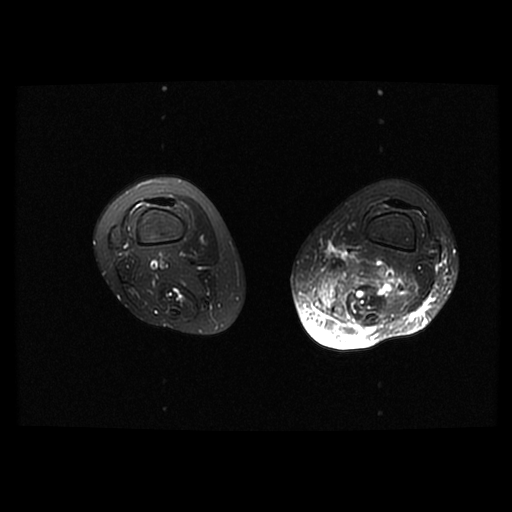
MRI of an extremity soft-tissue mass, one axial slice. Position 16 of 42 along the scan axis. T2-weighted fat-saturated. 6 mm slice thickness. 512 × 512 image matrix, field of view 420 × 420 mm. Female patient. Case-level facts recorded for this patient, not image findings: histological type: pleomorphic leiomyosarcoma; grade: high; site of the primary tumour: left thigh.
Annotated regions visible in this slice (outlined manually by an expert reader):
- gross tumour volume including surrounding oedema: bounding box [x1, y1, x2, y2] px = [311, 253, 411, 314]